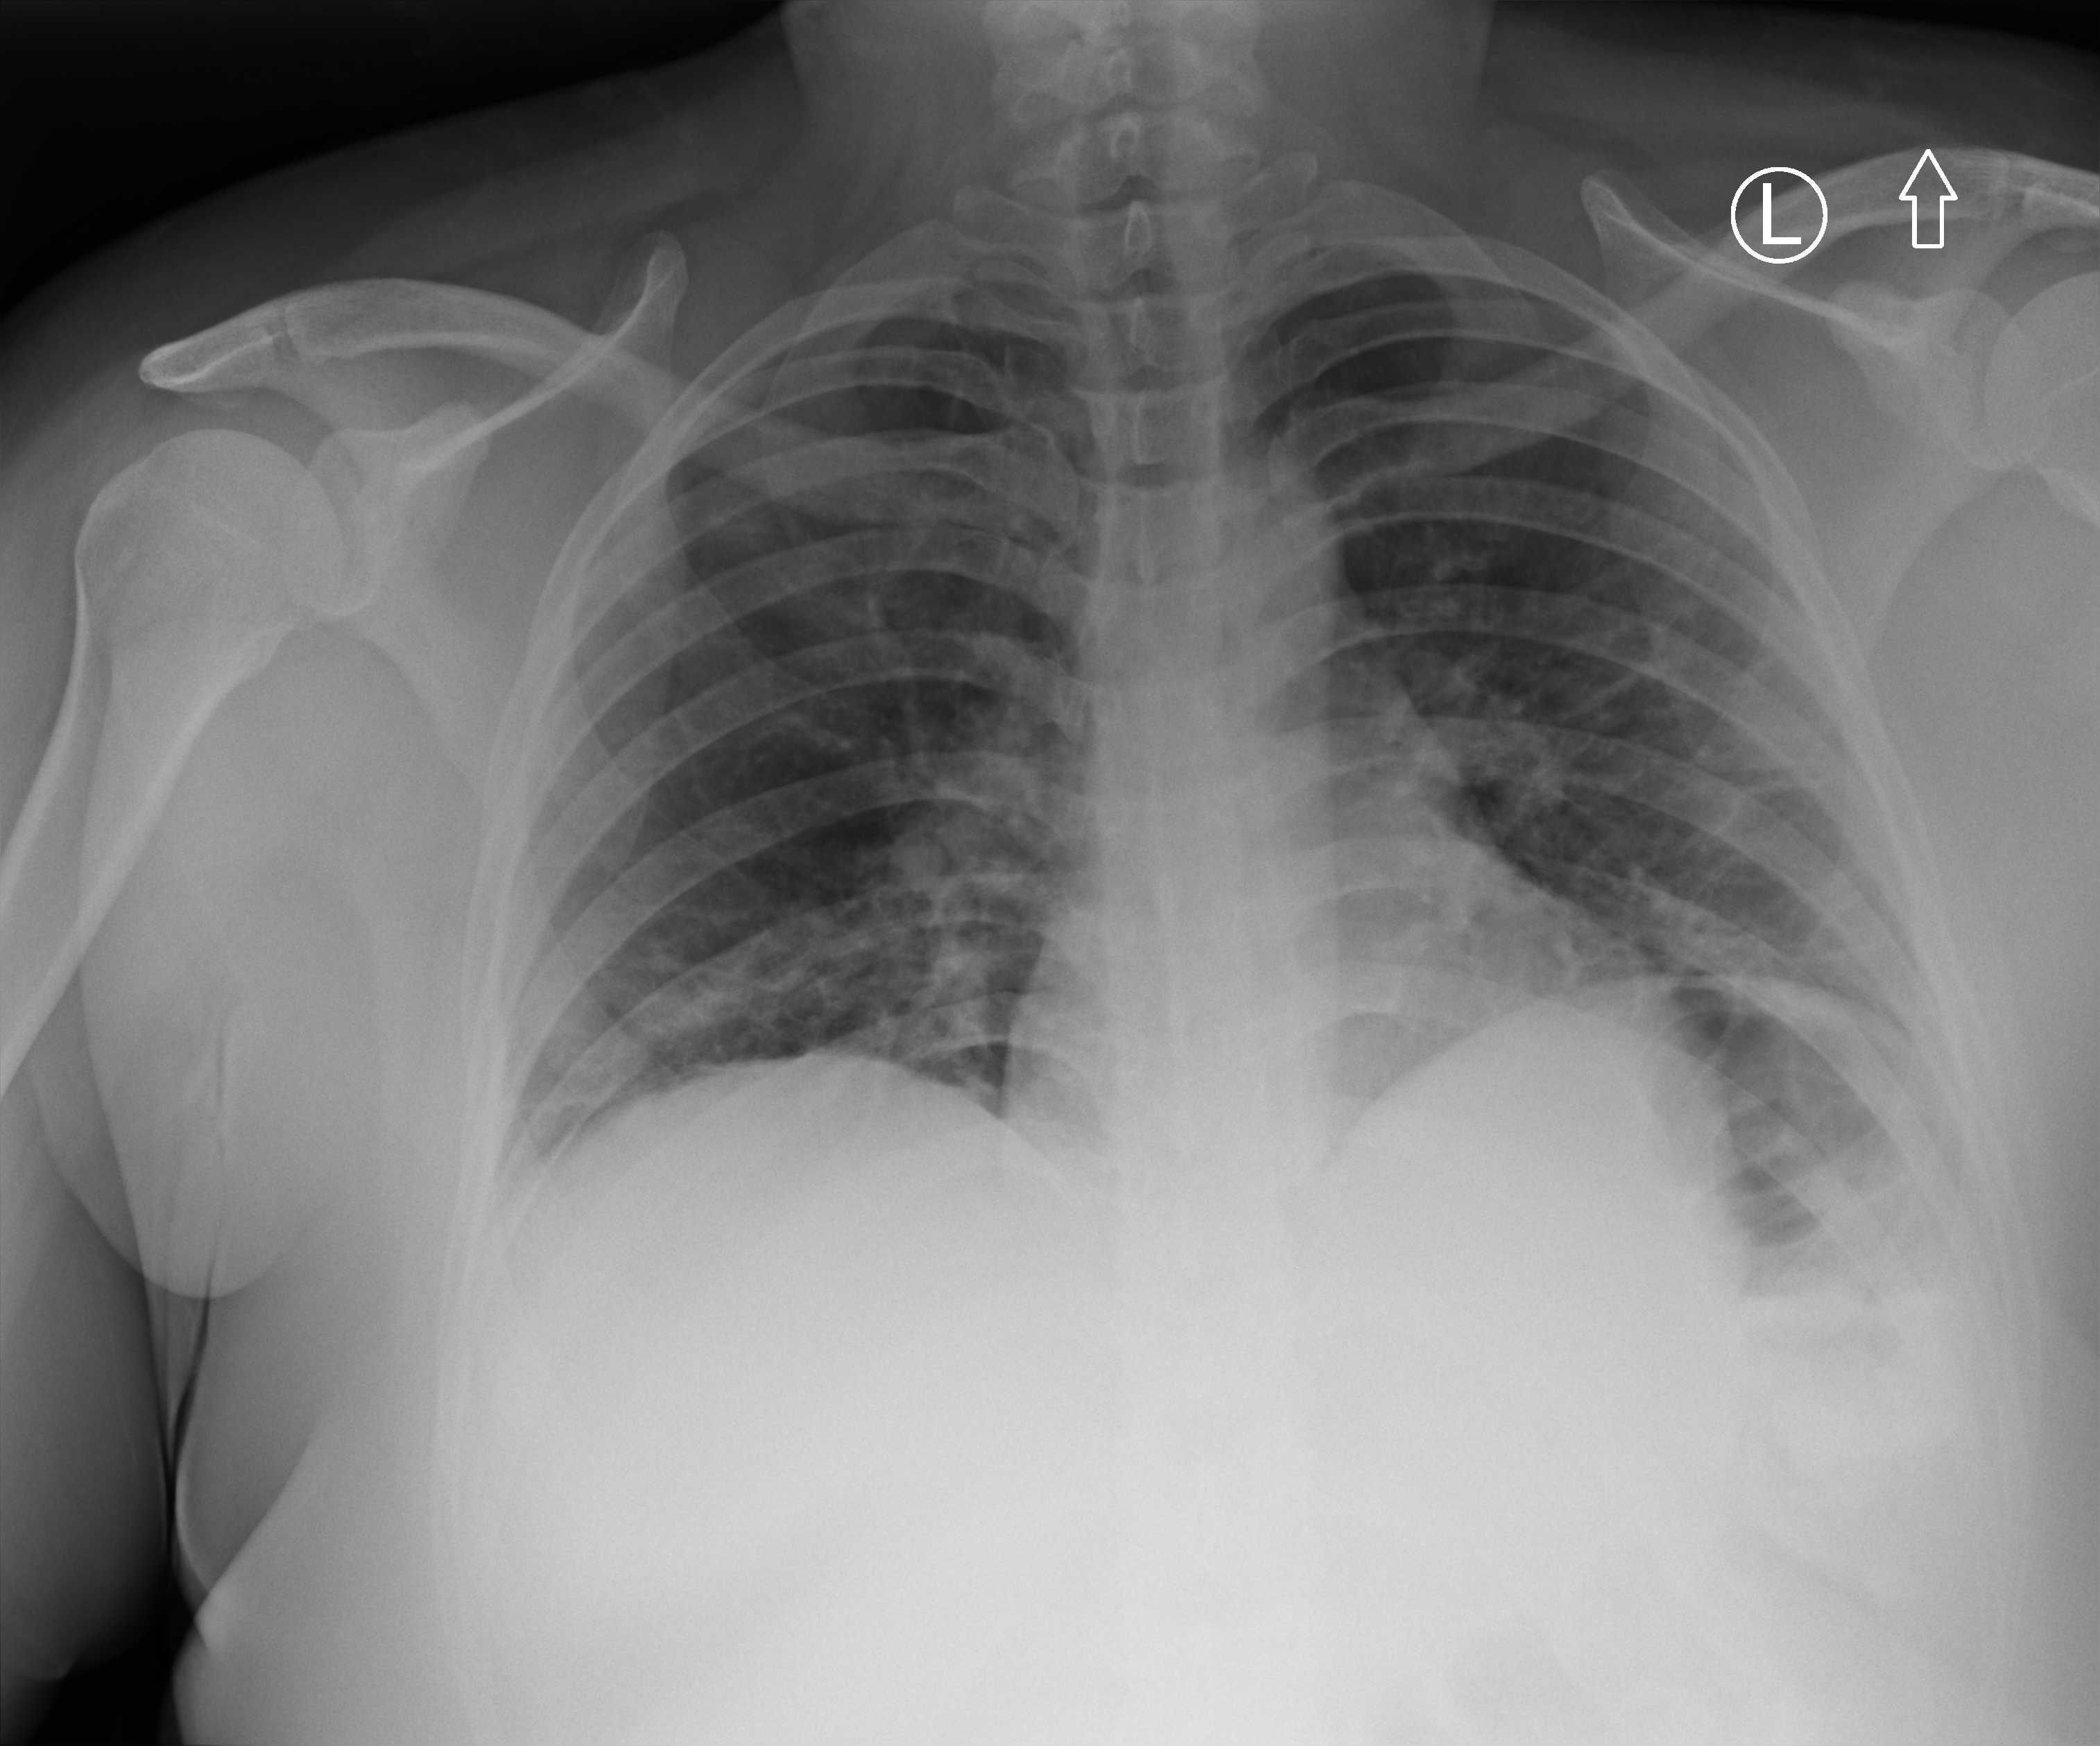
Chest X-ray (portable), anteroposterior (AP) projection. Patient hospitalised with COVID-19; female, aged 18–59 years.
Admission-level facts for this patient (not findings on this image; timing relative to this image not recorded): mechanically ventilated during this hospital stay: no.